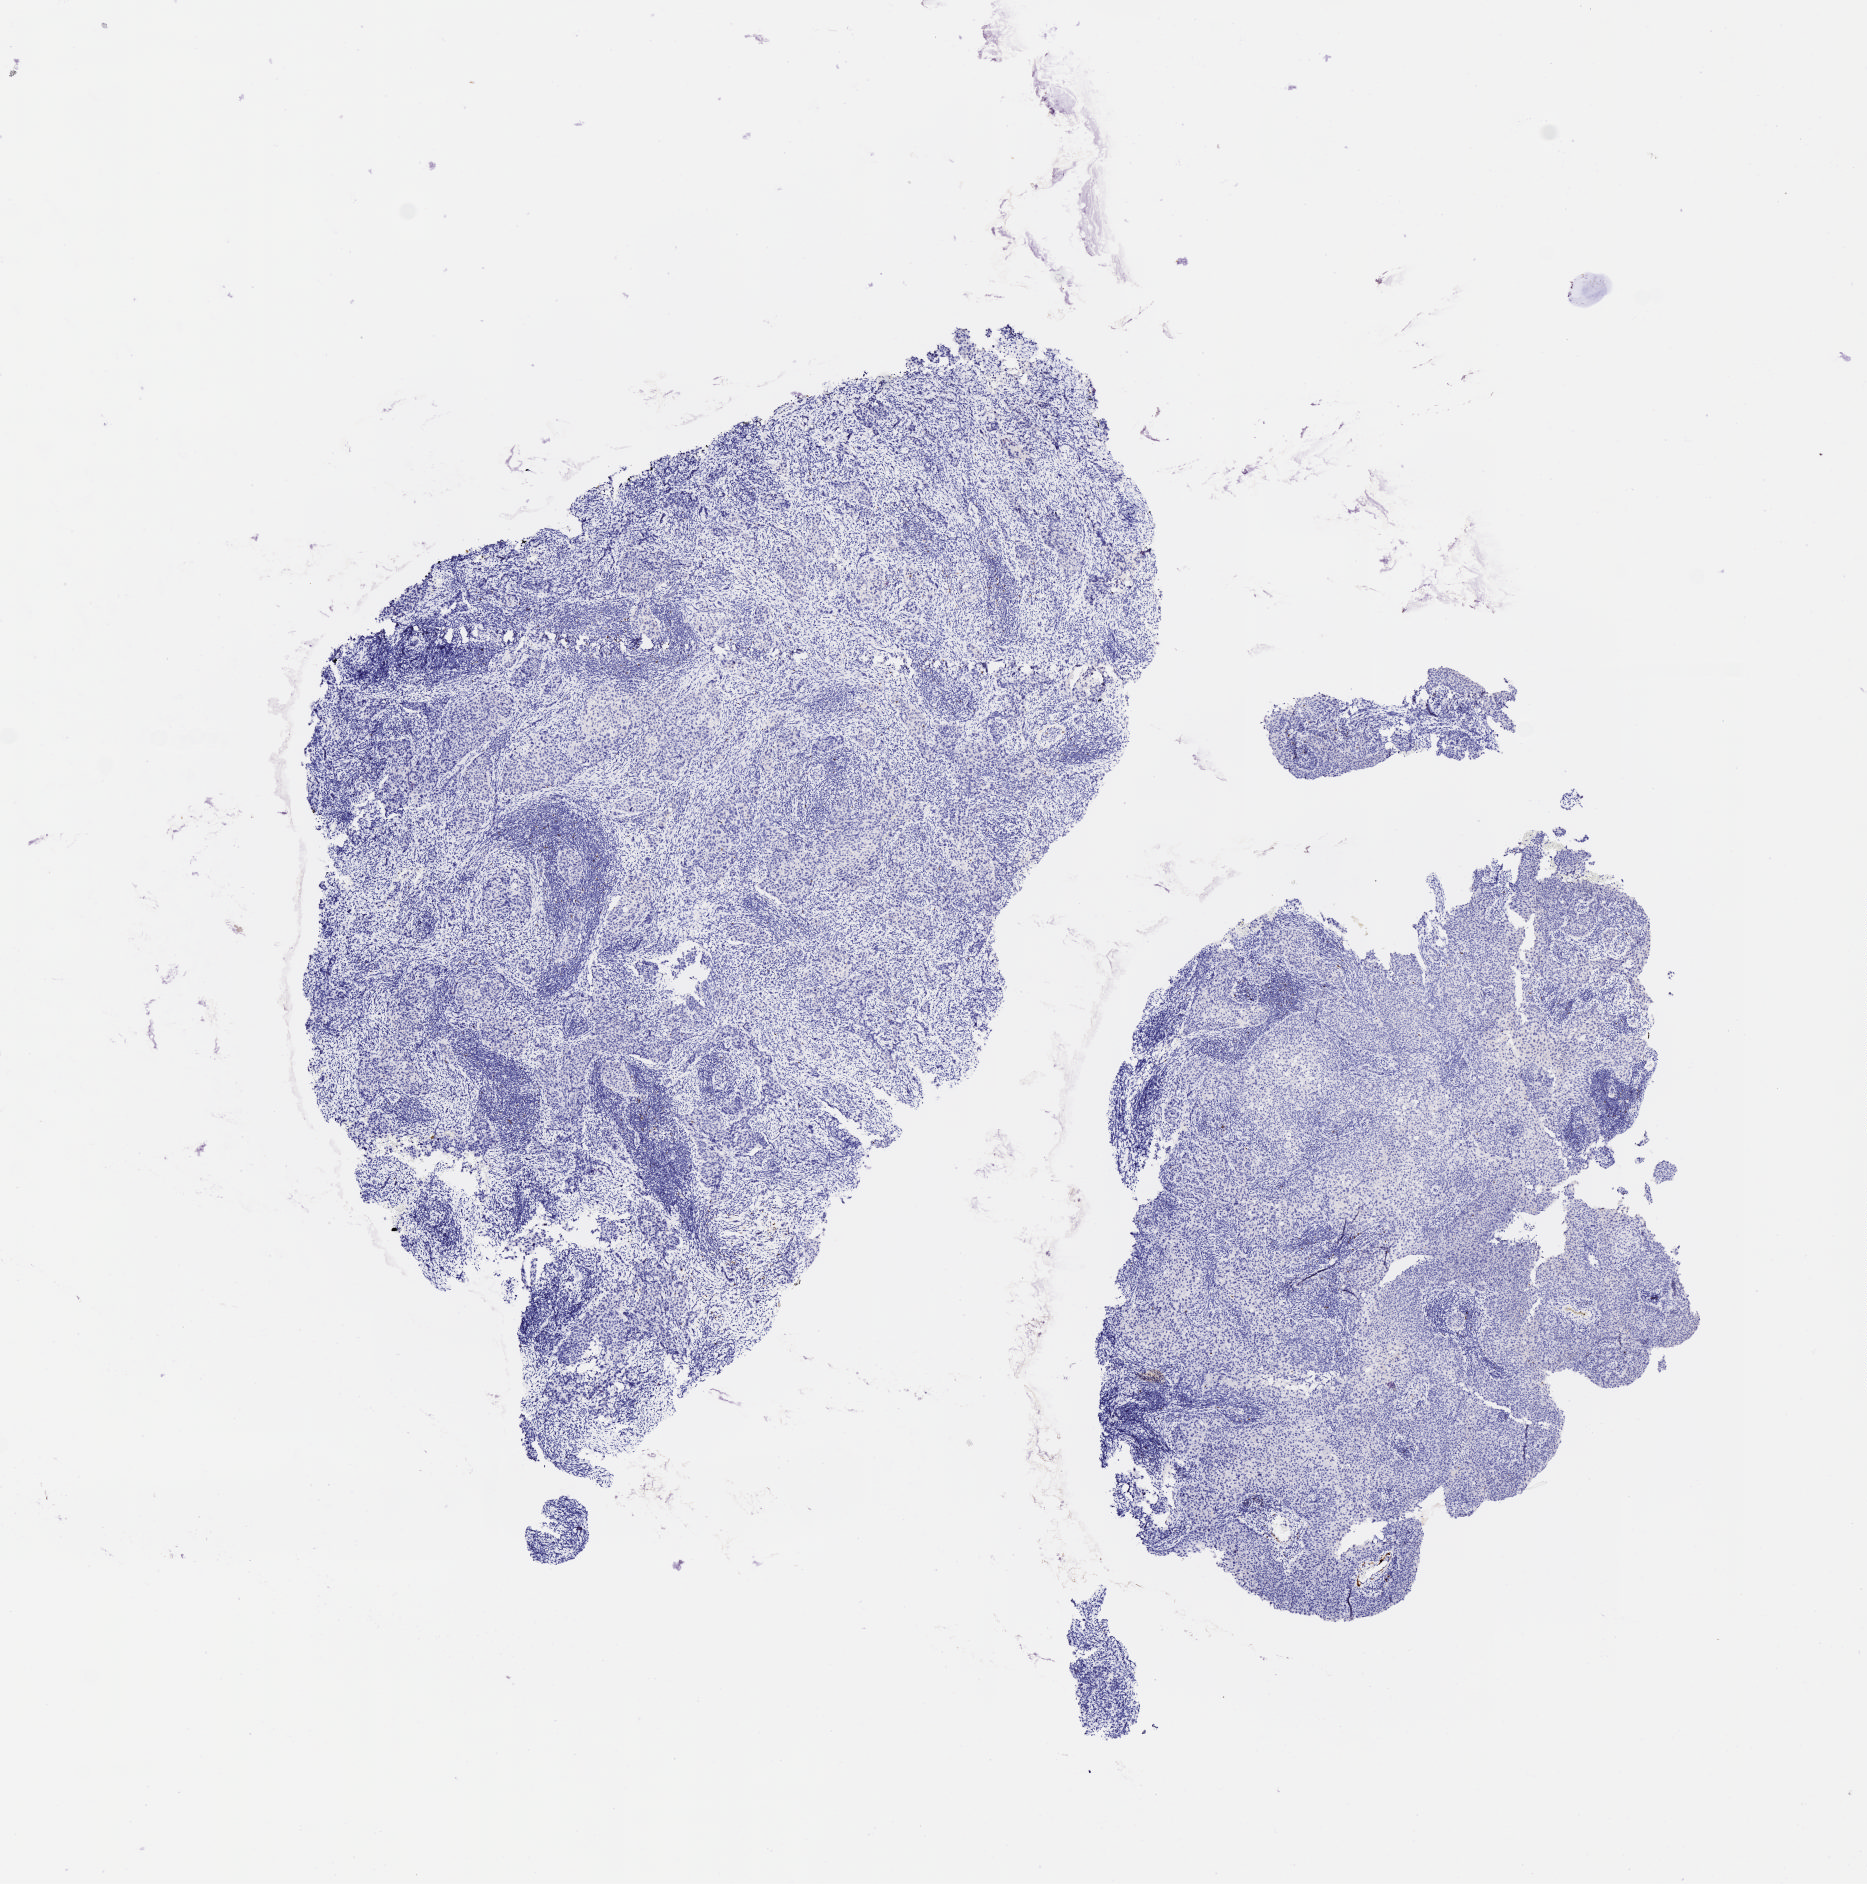
Immunohistochemistry (IHC) whole-slide image stained for p16 (p16INK4a) — a low-resolution overview of the entire scanned area, about 7.5 x 7.6 mm; specimen: tumor tissue; site: cervix. Patient: female, 74 years old.
Diagnosis: Squamous cell carcinoma, large cell, nonkeratinizing, NOS.